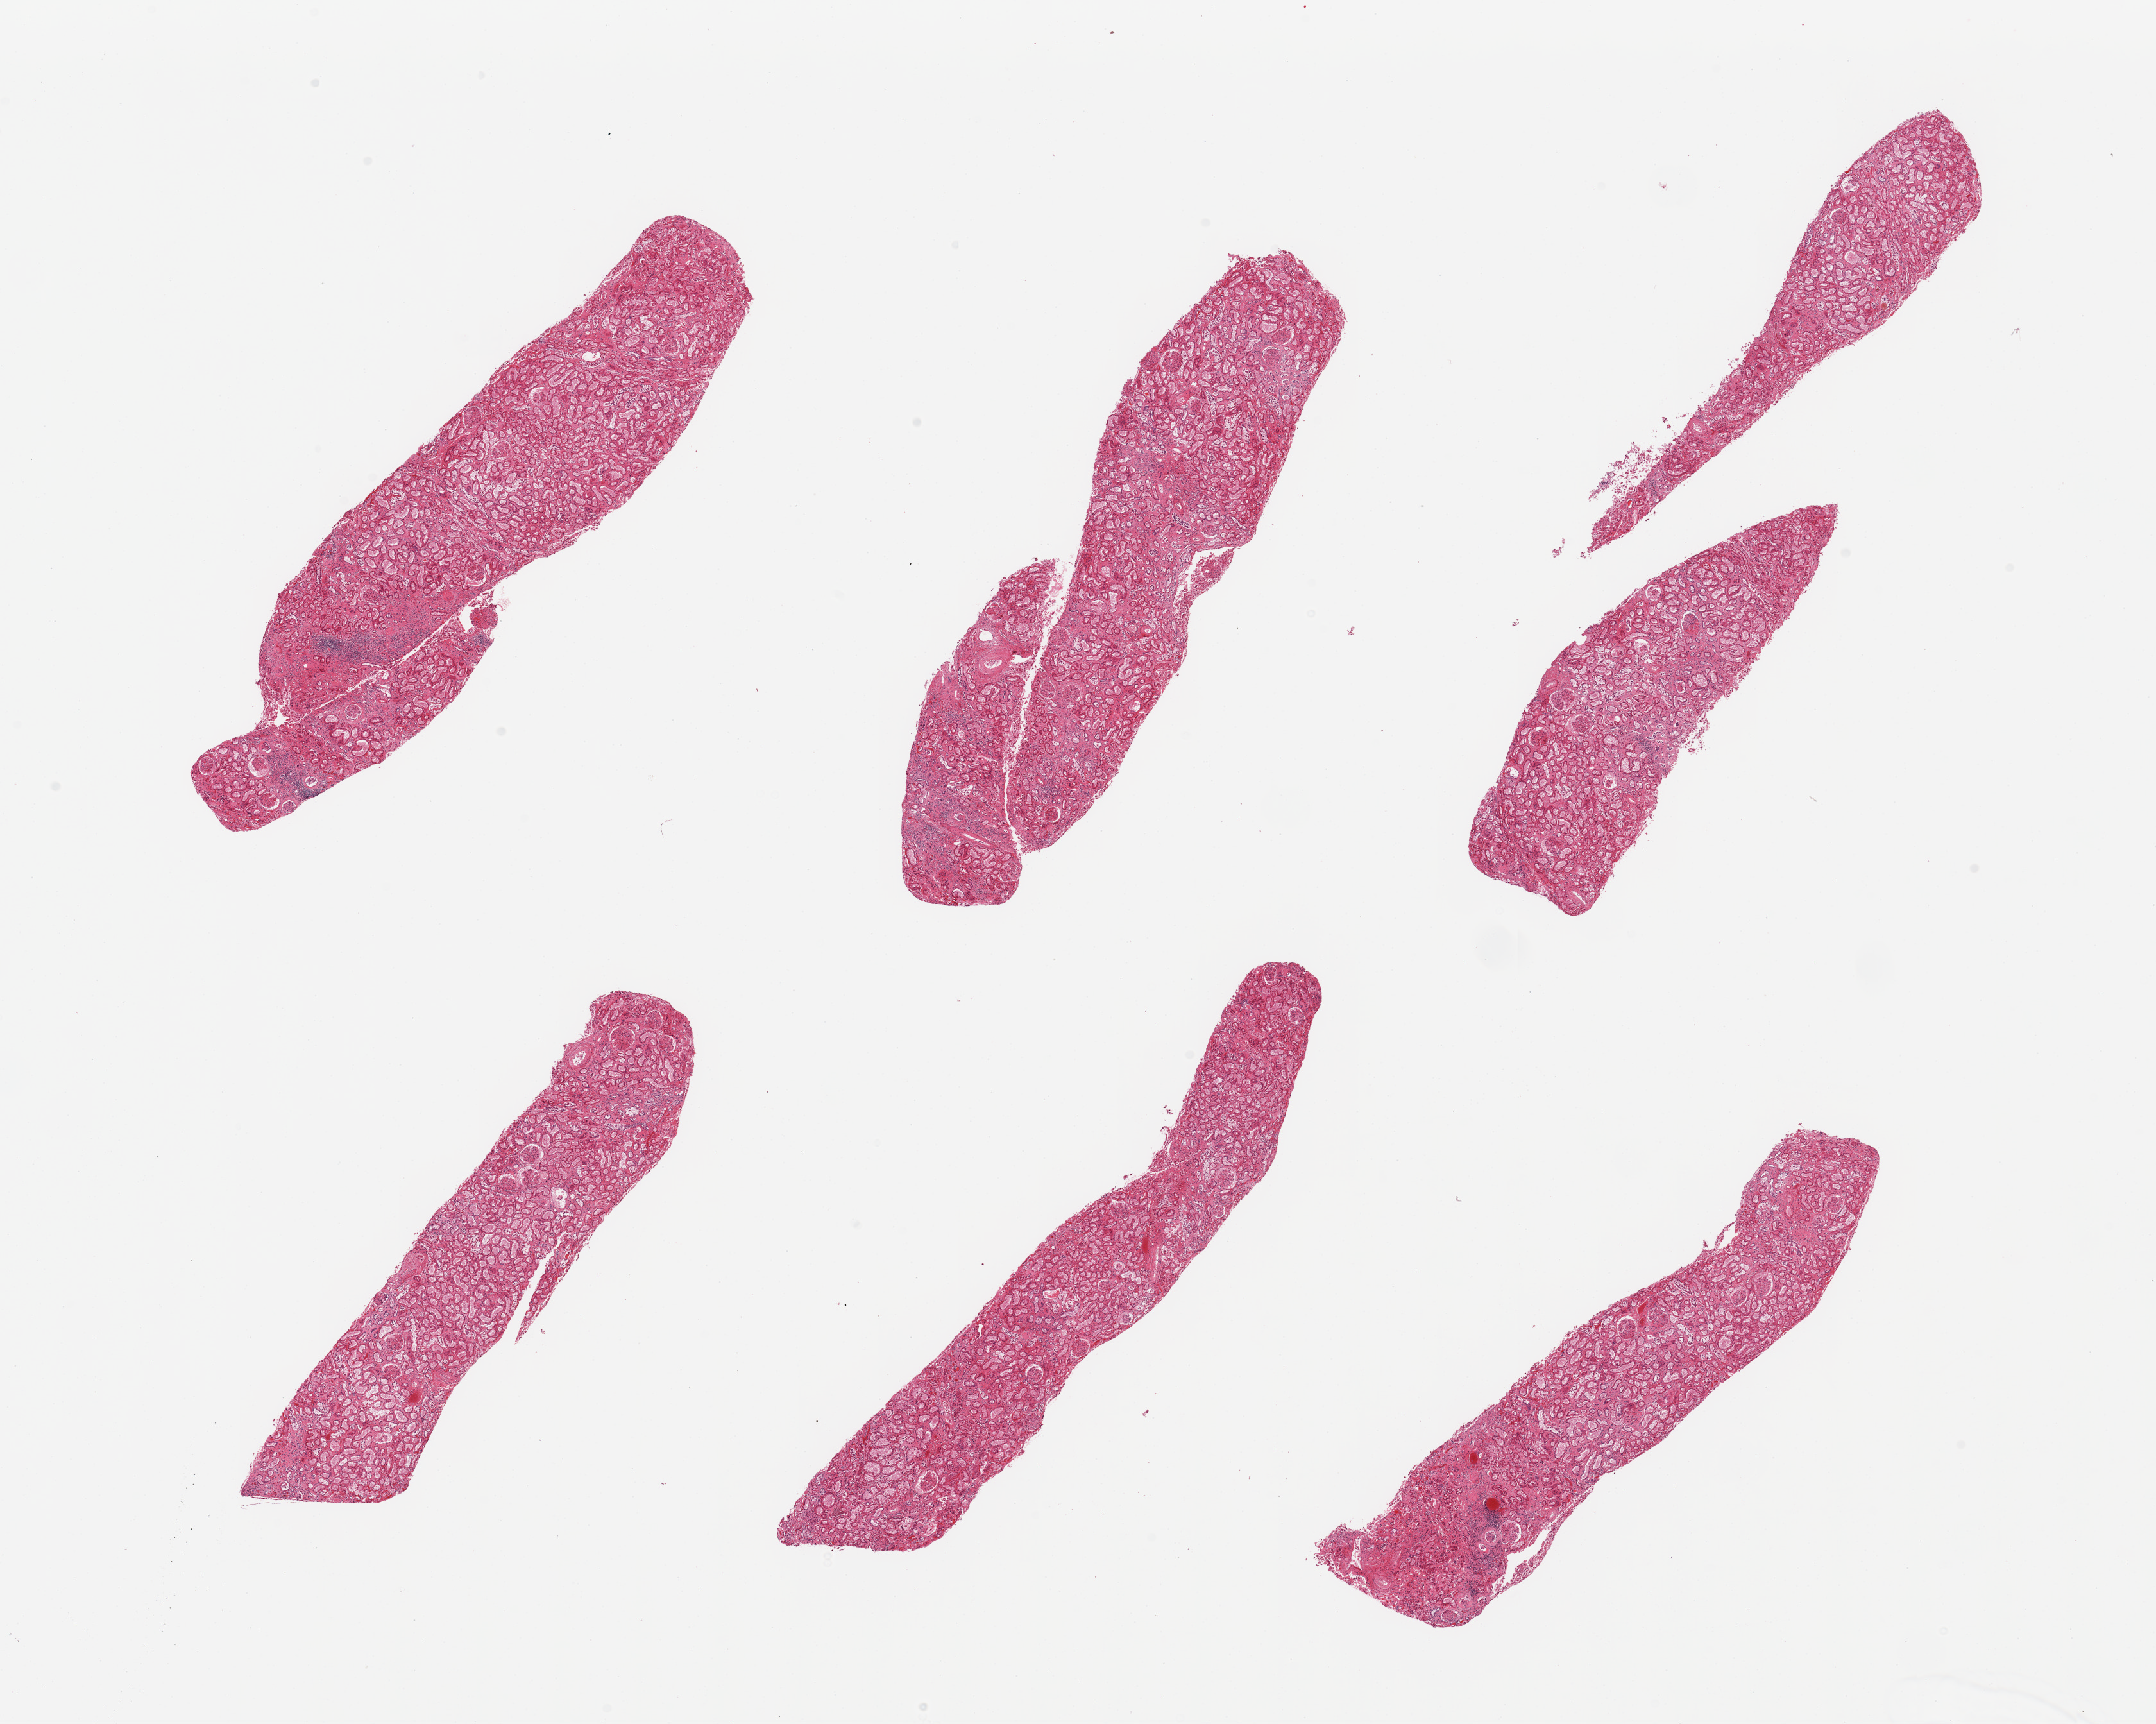
Hematoxylin and eosin (H&E) whole-slide image, brightfield, whole scanned area (about 26.6 x 21.2 mm) shown as a low-resolution overview. PAXgene-fixed, paraffin-embedded tissue. Section of renal cortex (target tissue). Tissue donor sample. Donor: male.
Review note (as recorded): 6 pieces; cortex with focal interstitial fibrosis and chronic inflammation, sclerotic glomeruli and hyalinized vascular walls (diabetic nephropathy).